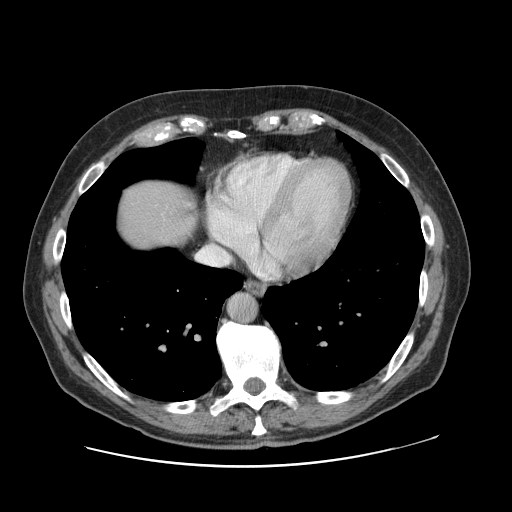
Contrast-enhanced abdominal CT, one axial slice; position 116 of 138 along the scan axis; intravenous contrast given; soft-tissue window (W 400 / L 40 HU); 2.5 mm slice thickness; 512 × 512 image matrix. Male patient, age 71 years. From the clinical record (not read from this slice): diagnosis: colorectal cancer liver metastases, imaged before liver resection; multiple liver metastases: no; largest metastasis: 3.3 cm; disease in both lobes: no.
Annotated regions visible in this slice (manually delineated by an expert):
- liver: bounding box <115,178,197,252> (left, top, right, bottom; pixels)
- planned liver remnant (the part of the liver to remain after resection): <115,179,196,252>